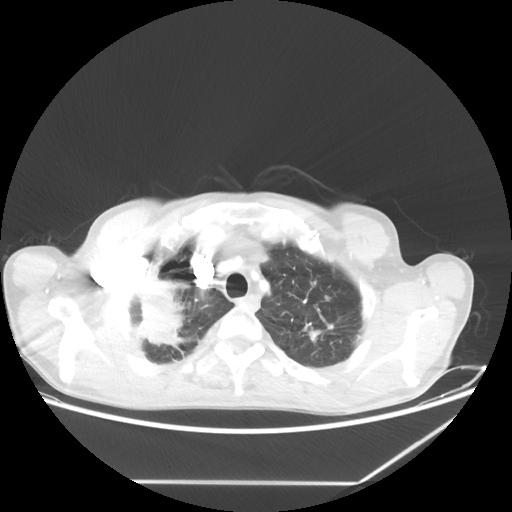
Chest CT, one axial slice; position 55 of 65 along the scan axis; lung window (W 1500 / L -600 HU); 5 mm slice thickness; 512 × 512 image matrix. Male patient, age 68 years. From the clinical record (not read from this slice): clinical TNM (as recorded): T3 N3 M0.
Outlined on this slice (rectangle marked by the reading radiologist):
- lung tumour (recorded histology: adenocarcinoma): bounding box [x1, y1, x2, y2] px = [139, 268, 195, 351]